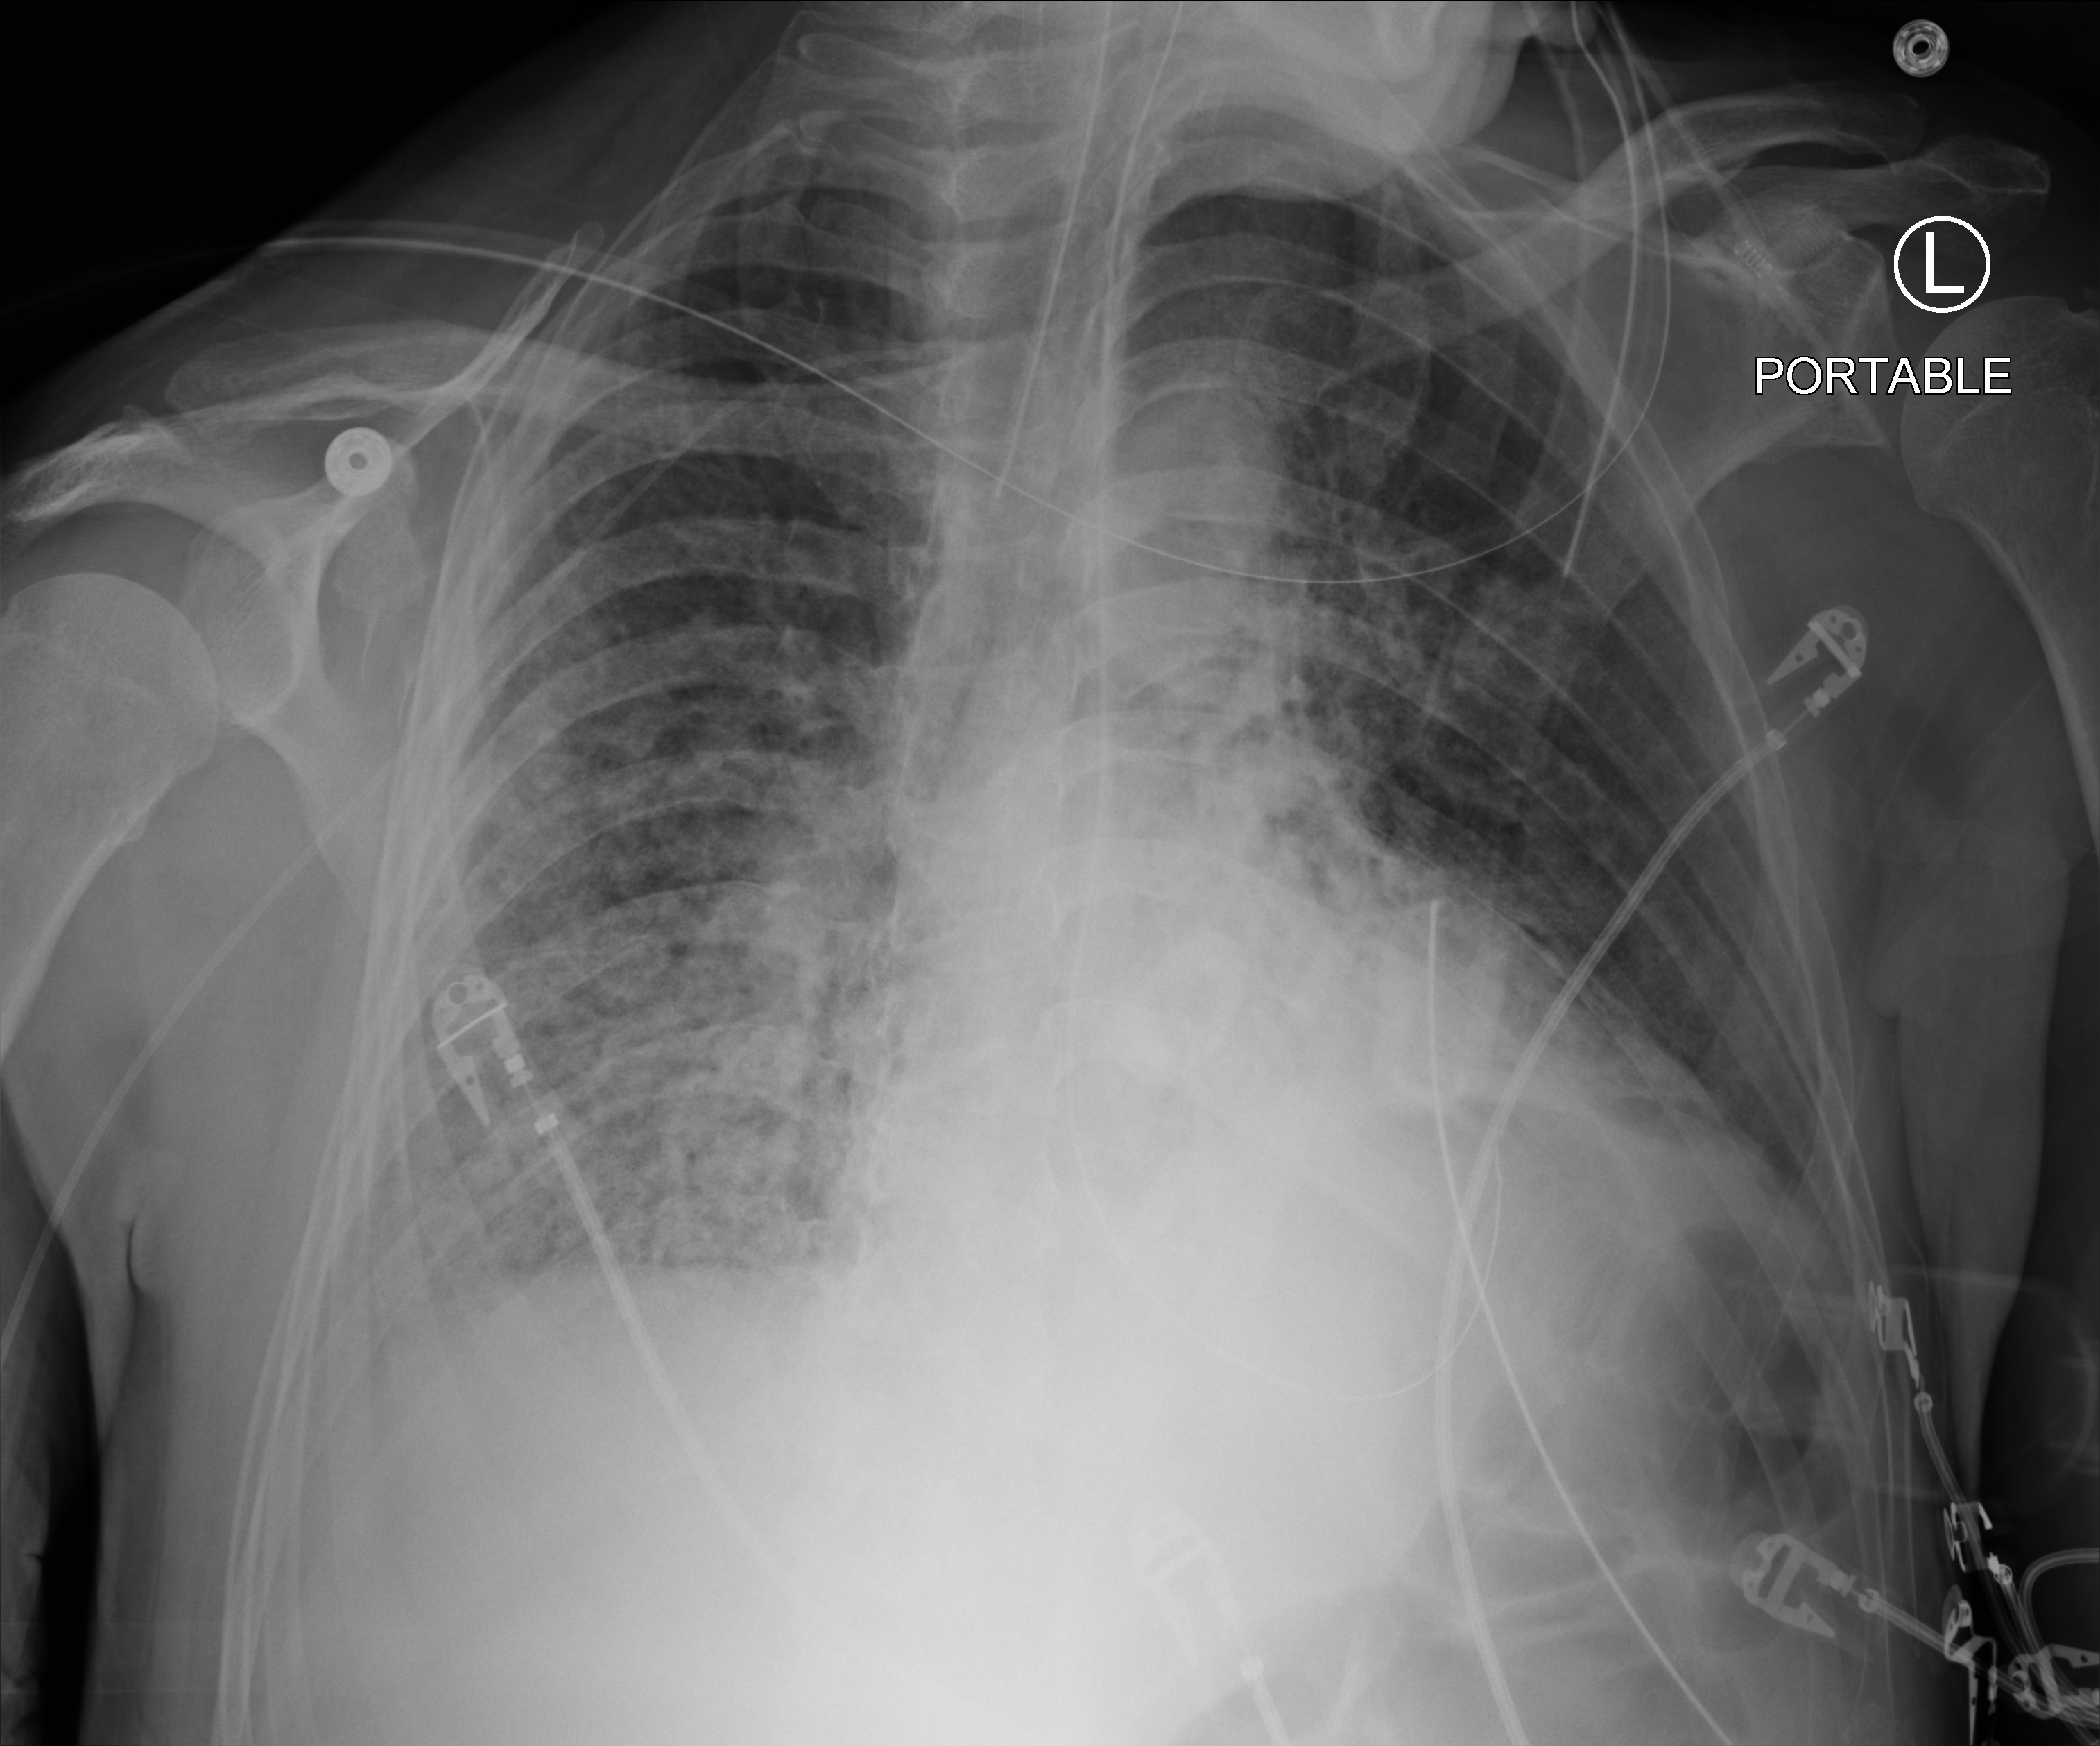
Portable chest radiograph. Male patient hospitalised with COVID-19, age 60–74 years.
Admission-level facts for this patient (not findings on this image; timing relative to this image not recorded): admitted to intensive care during this hospital stay: yes; other chronic lung disease (admission record): no.